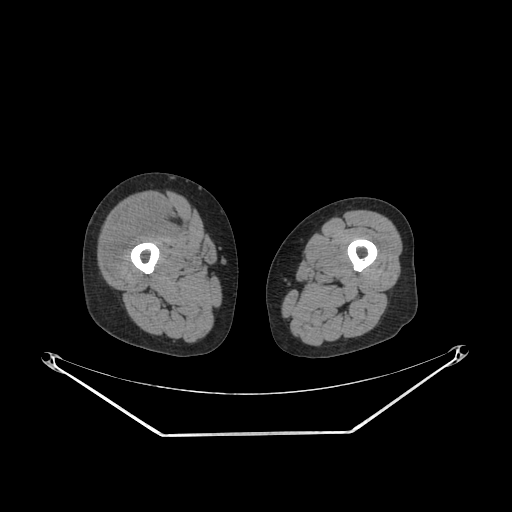
CT of an extremity soft-tissue mass (from a PET/CT study), one axial slice; slice 227 of 311 in the series (ordered by position); 140 kVp; soft-tissue window (W 400 / L 40 HU); 3.75 mm slice thickness; 512 × 512 image matrix. Female patient. From the clinical record (not read from this slice): histological type: pleiomorphic undifferentiated sarcoma; grade: high; site of the primary tumour: right quadricep.
Annotated regions visible in this slice (expert contour drawn on MRI and transferred to this co-registered scan by the dataset authors):
- tumour plus oedema (research contour): bounding box (x1, y1, x2, y2) in pixels: (105, 201, 175, 275)